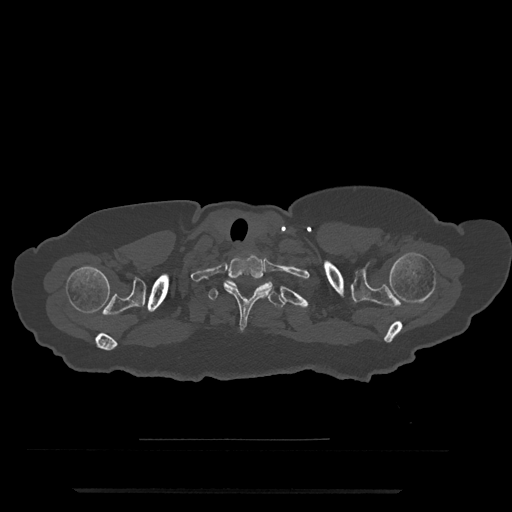
CT including the spine, one axial slice; position 700 of 797 along the scan axis; bone window (W 1800 / L 400 HU); 512 × 512 image matrix, field of view 440 × 440 mm. Patient: female, 51 years. From the clinical record (not read from this slice): primary cancer: neuro.
Outlined on this slice (semi-automatic segmentation, software-assisted and operator-edited):
- T1 vertebra: bounding box <223,255,274,331> (left, top, right, bottom; pixels)
- T2 vertebra: <209,279,286,309>